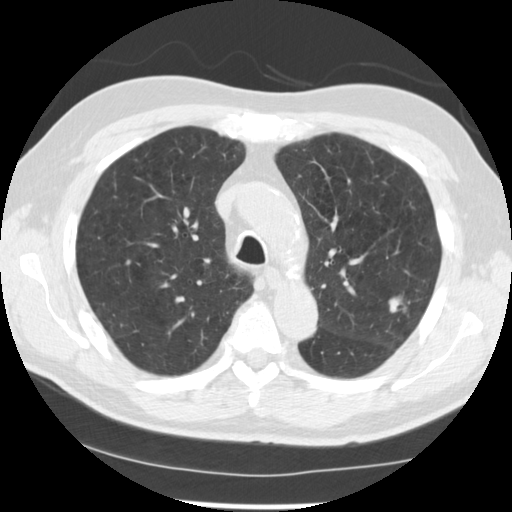
Low-dose screening chest CT, axial slice, baseline annual screen, lung window (W 1500 / L -600 HU), 2.5 mm slice thickness, standard (soft-tissue) reconstruction kernel (STANDARD), 120 kVp. Male participant, aged 71 years at enrolment.
- Expert reader's lesion annotation, bounding box [x1, y1, x2, y2] px = [375, 283, 426, 331].
- The screening reader recorded 2 non-calcified nodules or masses ≥4 mm on this exam (left upper lobe, left upper lobe); which of them this box marks is not recorded.
- Participant outcome: lung cancer diagnosed 37 days after this screen — adenocarcinoma, NOS, left upper lobe, poorly differentiated (G3), stage IIIB (AJCC 6th edition), 25 mm at pathology.